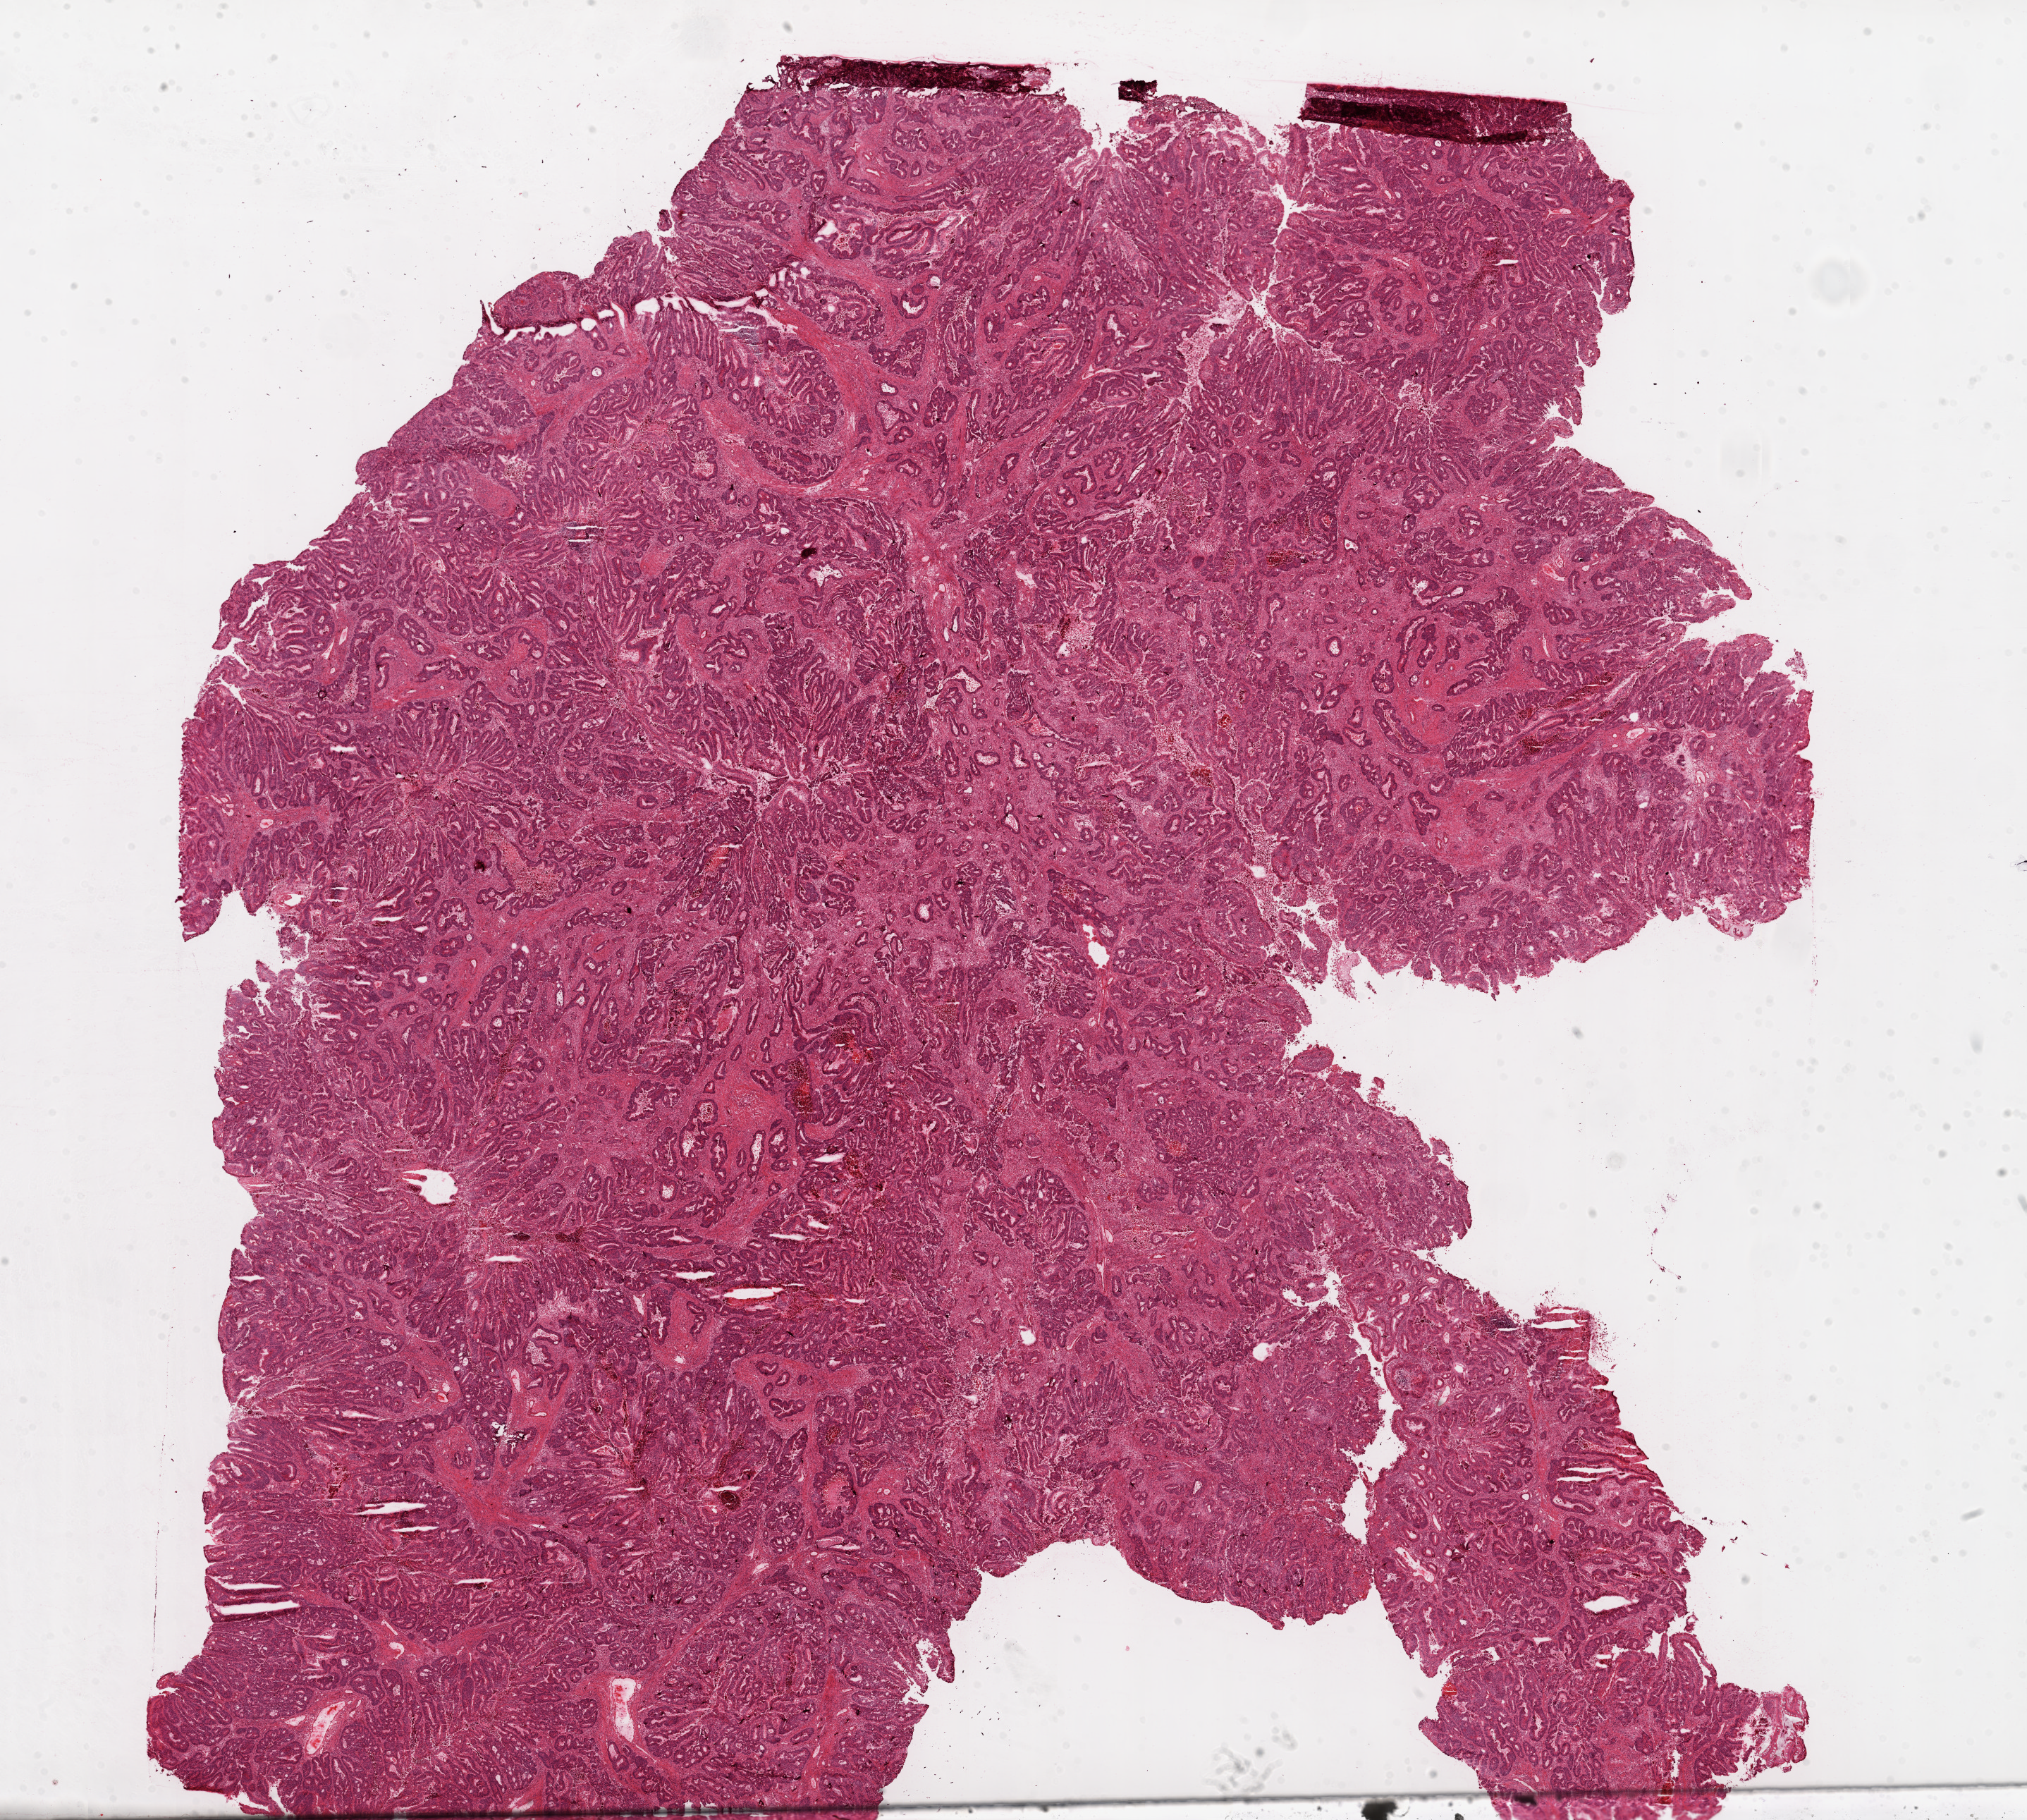
Whole-slide histology image, H&E-stained, shown as a low-resolution overview of the whole scanned area (about 23.1 x 20.7 mm, slide scanned at 20x); frozen section from the top of the tissue portion; primary tumour sample from the rectum. Patient: male, age at initial diagnosis 57 years. Pathologist review of this section (percent, as recorded): tumour cells 80%, tumour nuclei 75%, normal cells 0%, stromal cells 15%, necrosis 5%.
* TNM: T2 N0 M0
* histologic diagnosis: Adenocarcinoma, NOS (rectosigmoid junction)
* AJCC pathologic stage: I (7th edition)